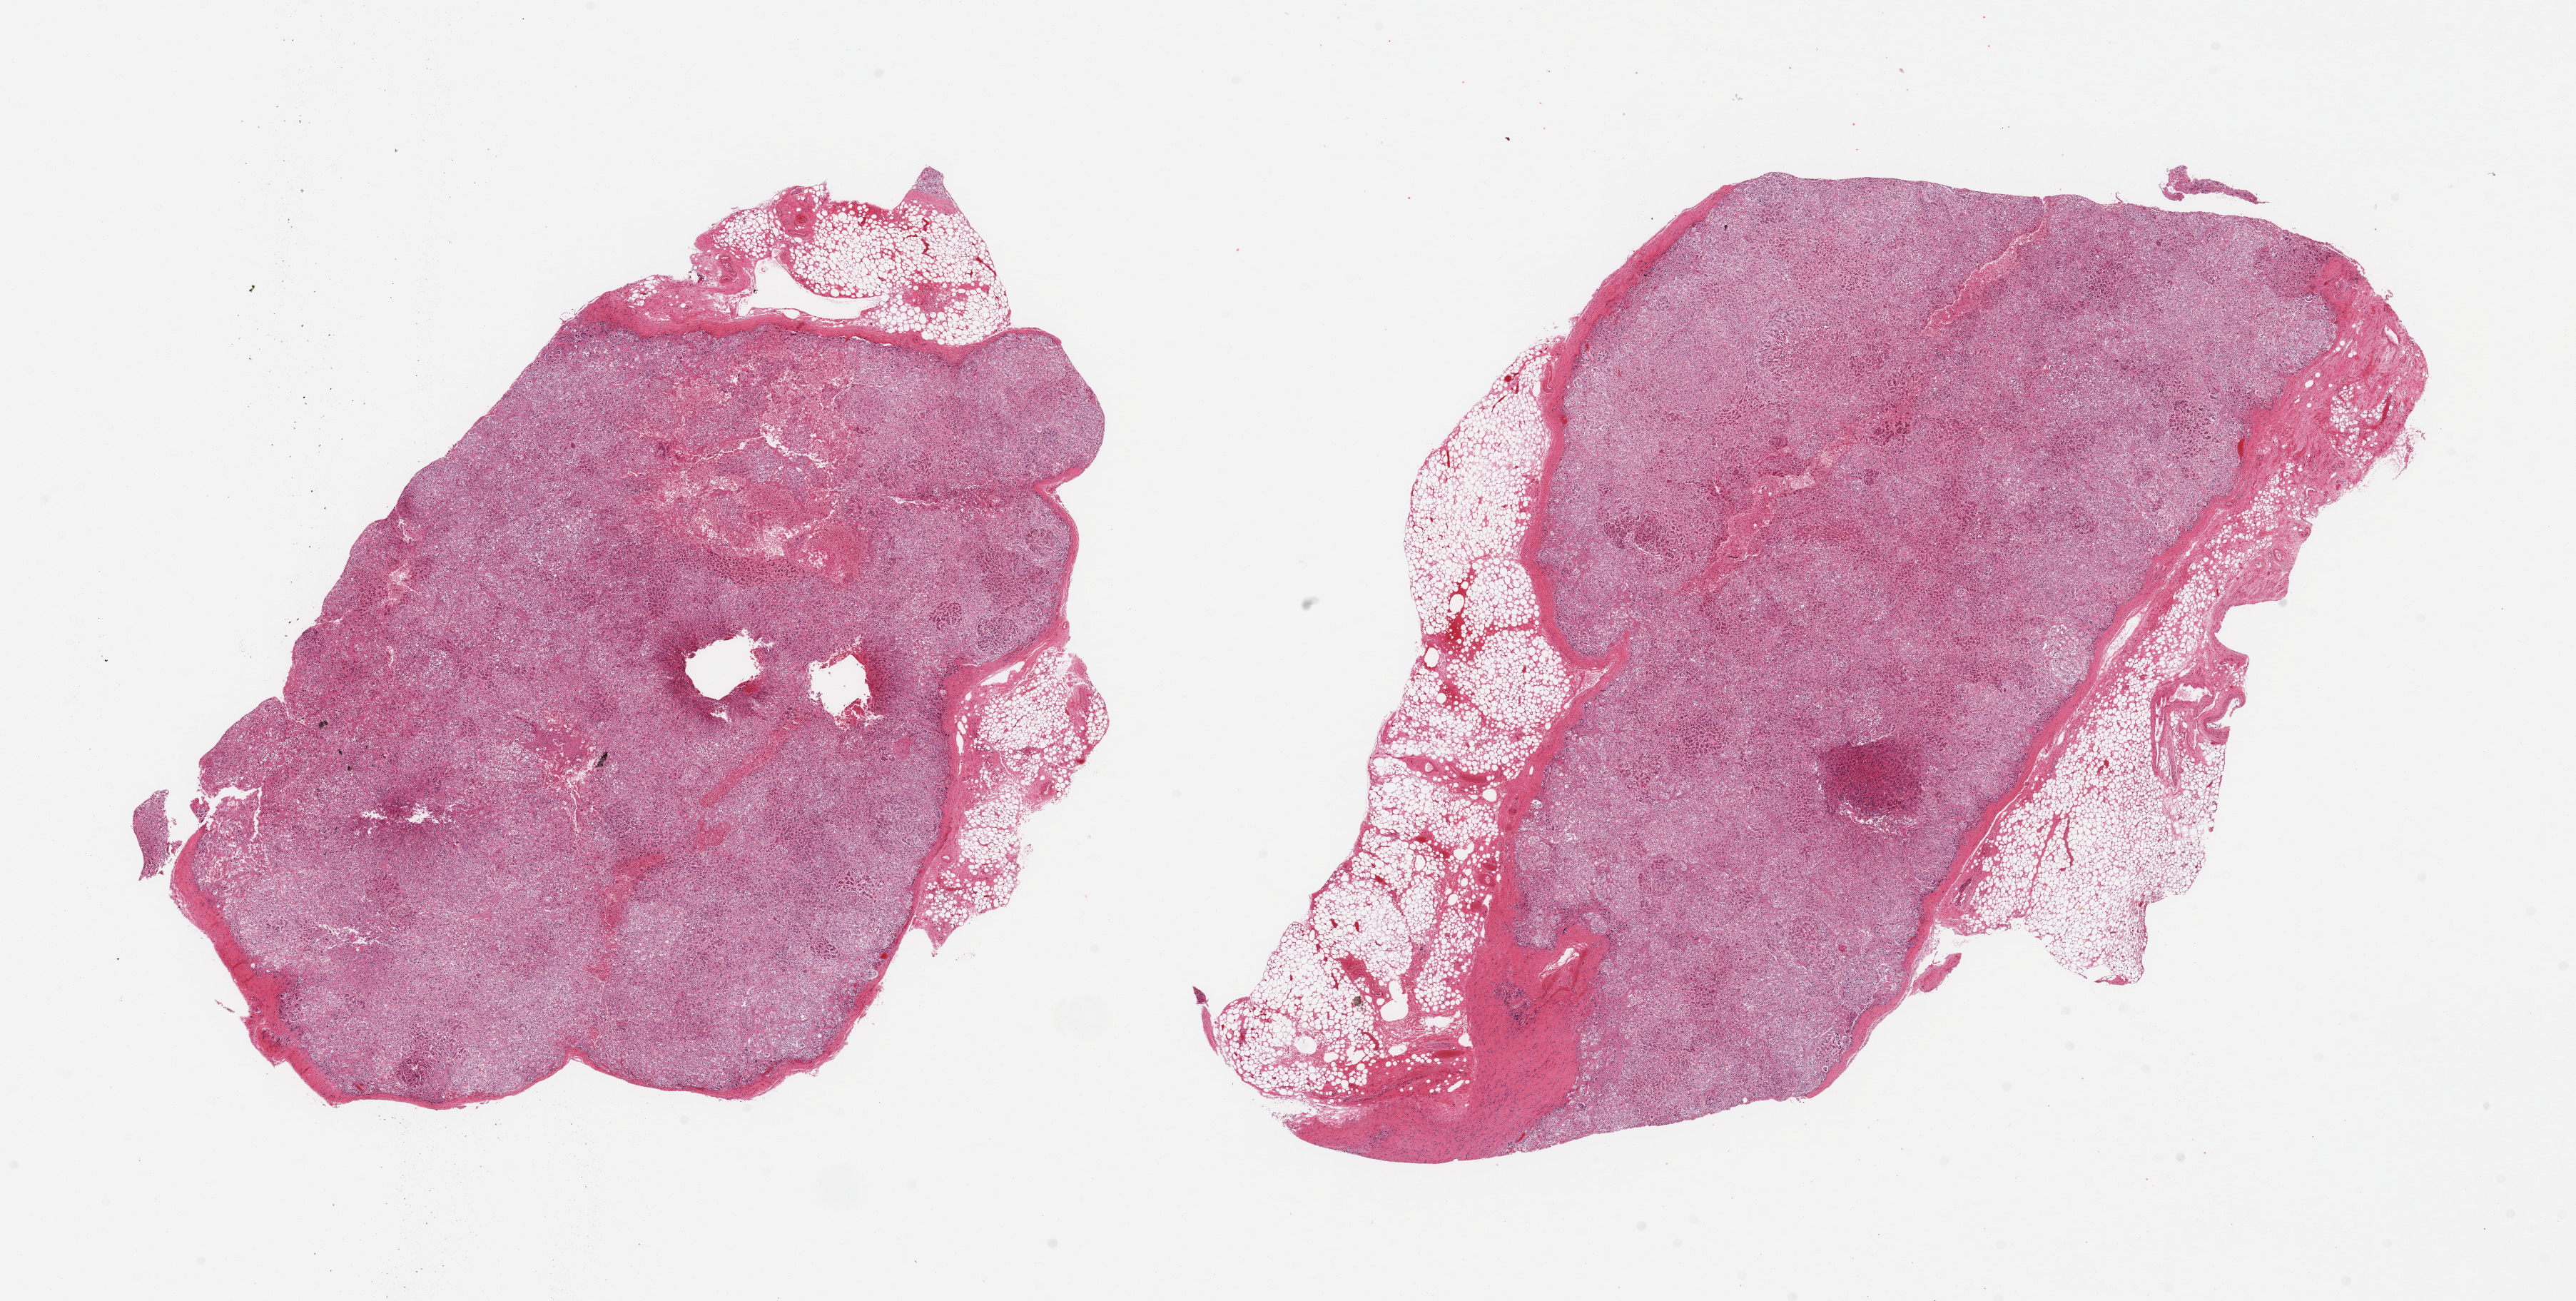
Digitized hematoxylin and eosin (H&E)-stained section, brightfield — a low-resolution overview of the entire scanned area, about 28.5 x 14.4 mm, PAXgene-fixed paraffin-embedded (PFPE) section, sampled site (target tissue): adrenal gland, donor tissue sample. Donor: male.
Review note (as recorded): 2 pieces, all cortex, few nubbins adherant fat up to 1-2mm.